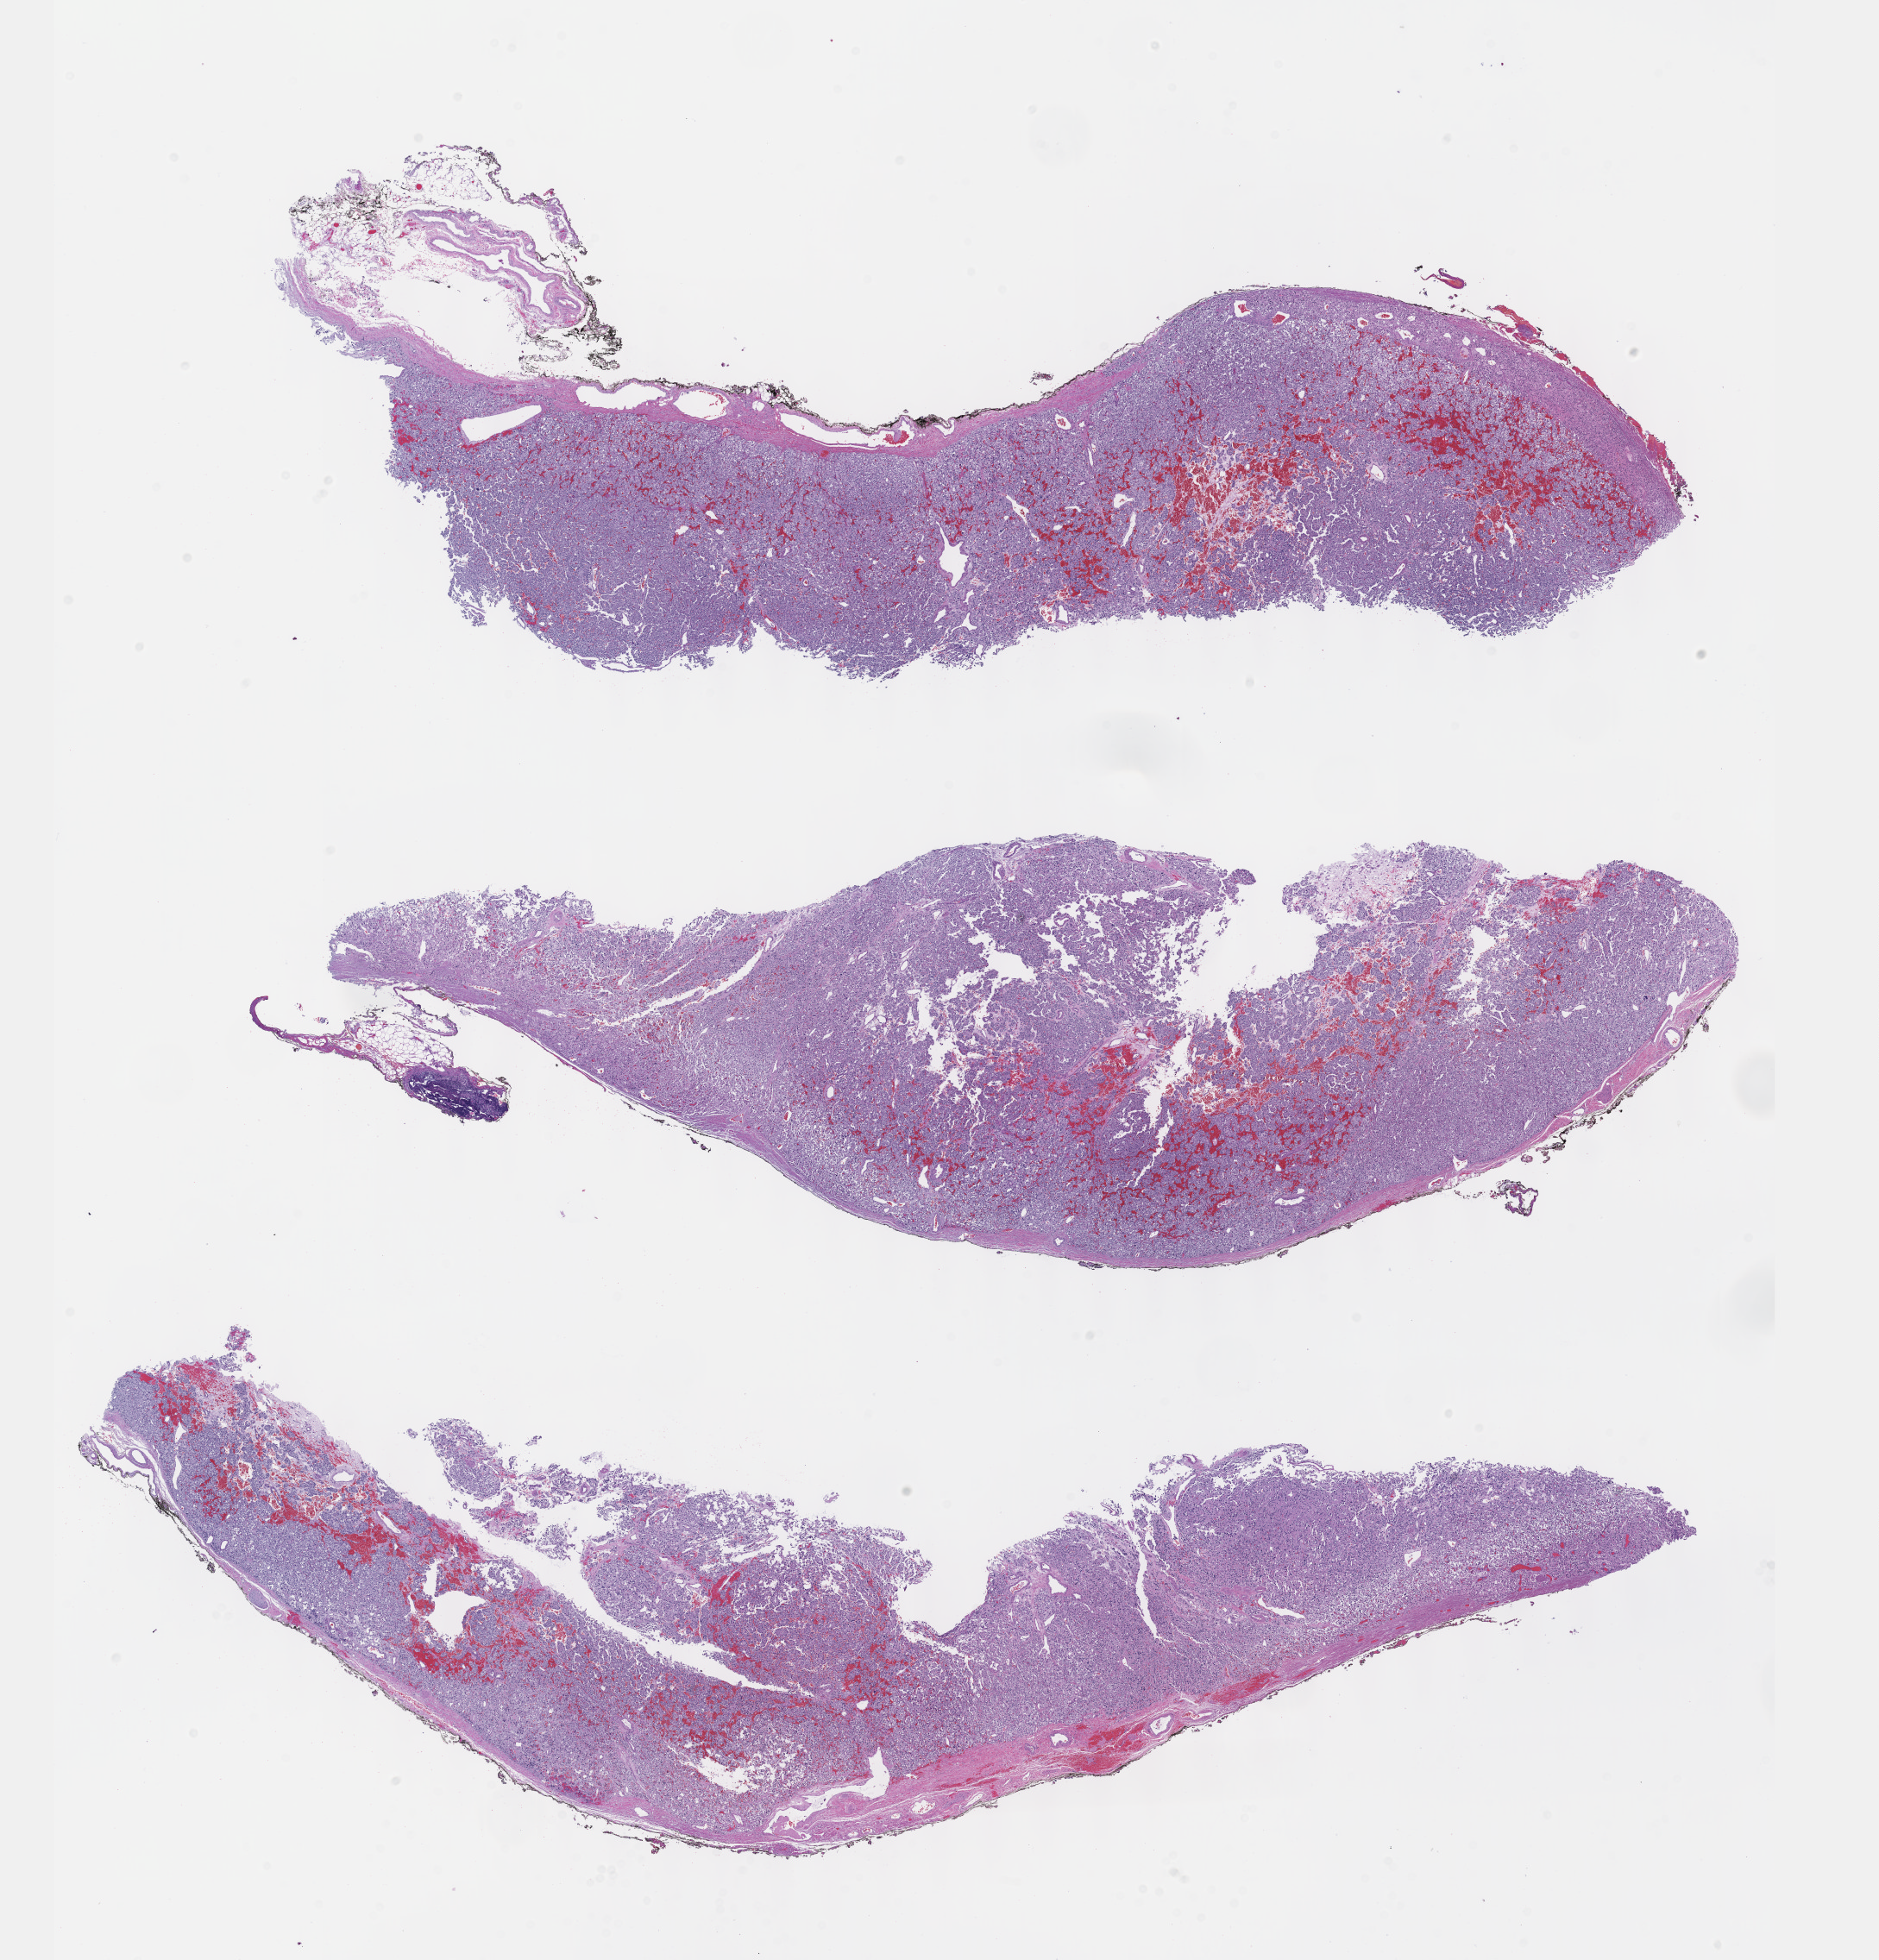
Digitized H&E-stained tissue section (whole slide), shown as a low-resolution overview of the whole scanned area (about 17.6 x 18.4 mm, acquisition: 40x scan); FFPE section; retroperitoneum and peritoneum, primary tumour sample. Male, age 30 years at initial diagnosis.
* pathologic diagnosis: Extra-adrenal paraganglioma, NOS (retroperitoneum)